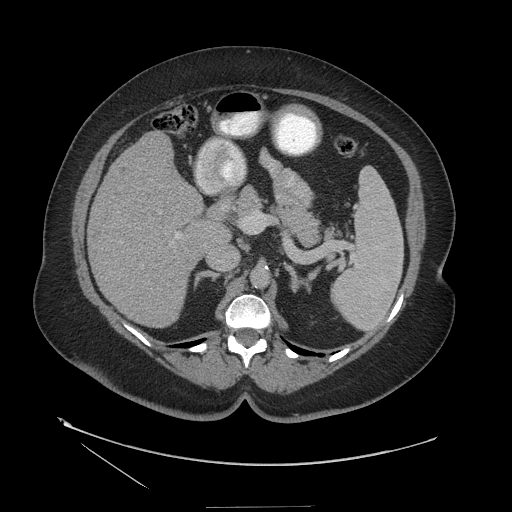
Contrast-enhanced abdominal CT (liver protocol), one axial slice; position 67 of 127 along the scan axis; reconstruction kernel STANDARD; soft-tissue window (W 400 / L 40 HU); 2.5 mm slice thickness; 512 × 512 image matrix, field of view 480 × 480 mm. From the clinical record (not read from this slice): diagnosis: hepatocellular carcinoma (patient treated with transarterial chemoembolisation; whether this scan precedes or follows treatment is not stated here); TNM stage (as recorded): Stage-II; Child-Pugh class: A; tumour nodularity: multinodular; tumour size: 3 cm.
Outlined on this slice (semi-automatically segmented with operator editing):
- liver parenchyma outside the tumour (the mass and vessels are separate outlines, so this box may not span the whole liver): bounding box <88,132,218,326> (left, top, right, bottom; pixels)
- liver vessels: <175,233,179,238>